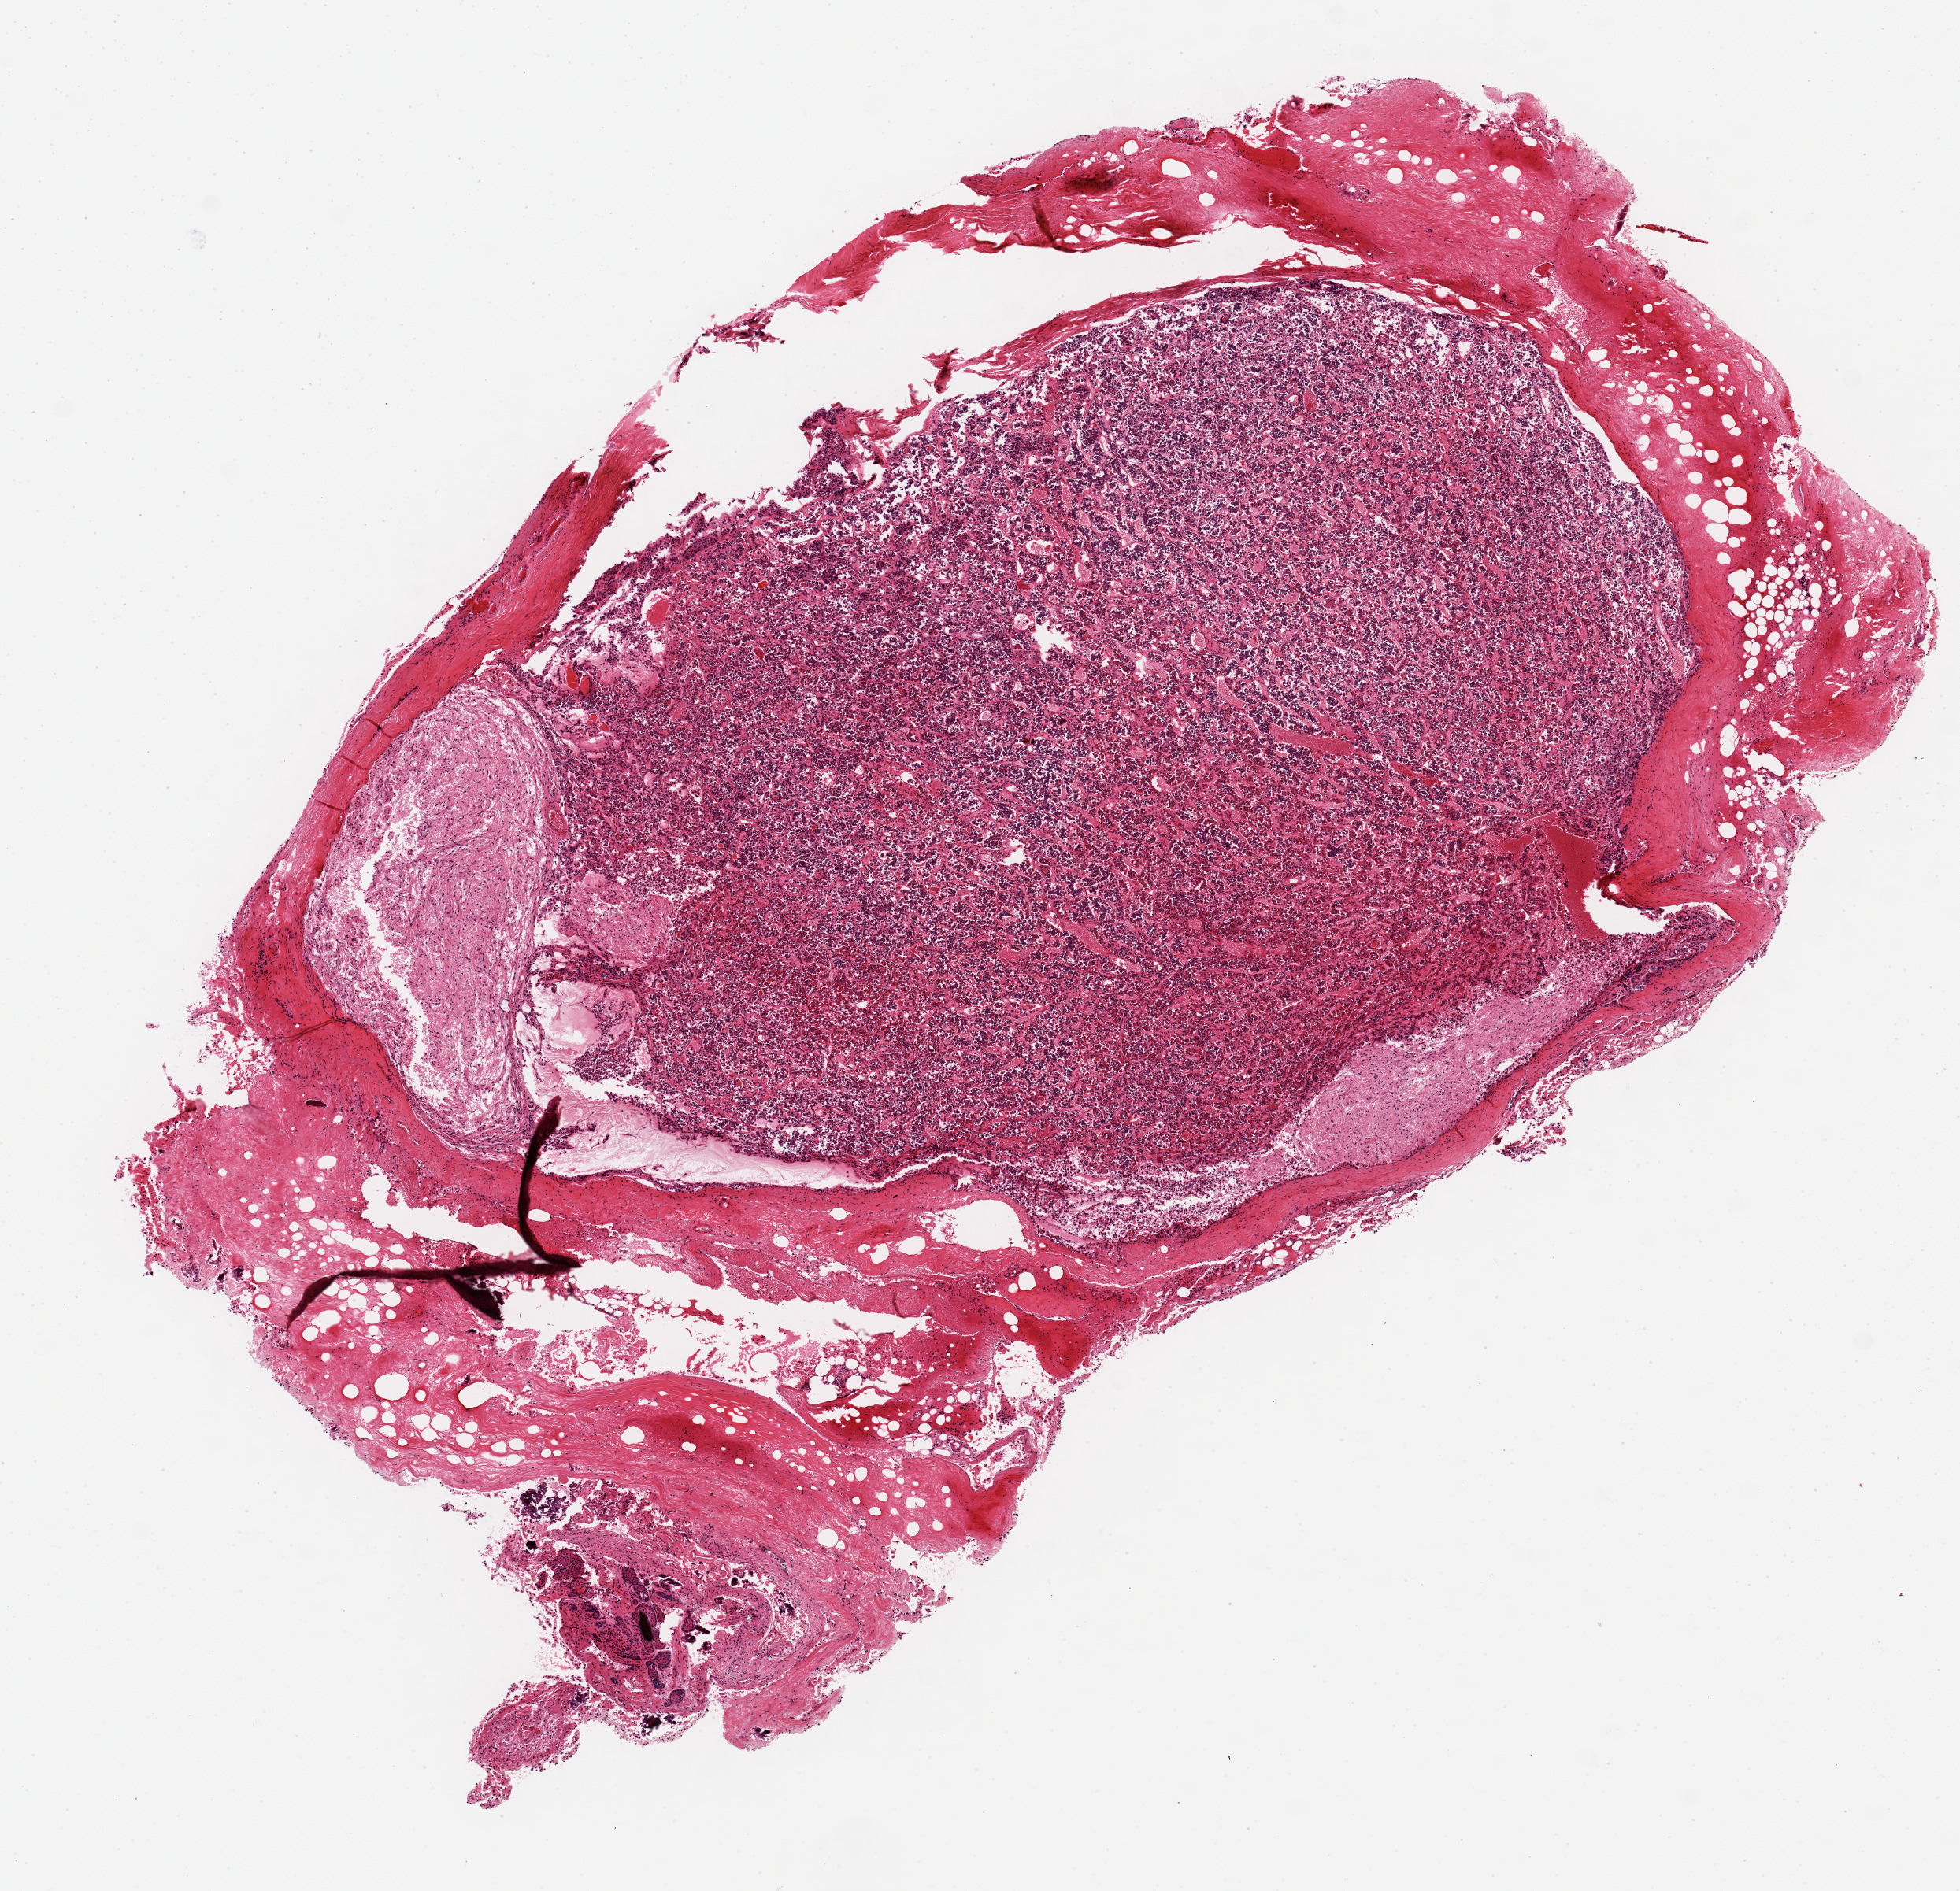
Digitized H&E-stained section, low-resolution overview of the scanned area, about 9.8 x 9.5 mm (slide scanned at 20x); PAXgene-fixed paraffin-embedded (PFPE) section; sampled site (target tissue): pituitary; donor tissue sample. Female donor.
Reviewer comment on this tissue sample: 1 aliquot, includes 6x4mm adenohypophysis and ~2.5x1.5mm neurohypophysis.